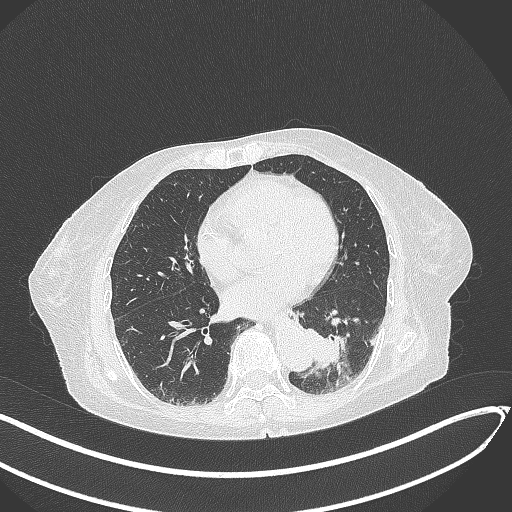
Chest CT, one axial slice; reconstruction kernel B70f; lung window (W 1500 / L -600 HU); 1 mm slice thickness; 512 × 512 image matrix. Patient: female, 82 years. From the clinical record (not read from this slice): clinical TNM (as recorded): T1b N0 M1.
Annotated regions visible in this slice (bounding box drawn by a radiologist):
- lung tumour (recorded histology: adenocarcinoma): bounding box <303,325,353,373> (left, top, right, bottom; pixels)